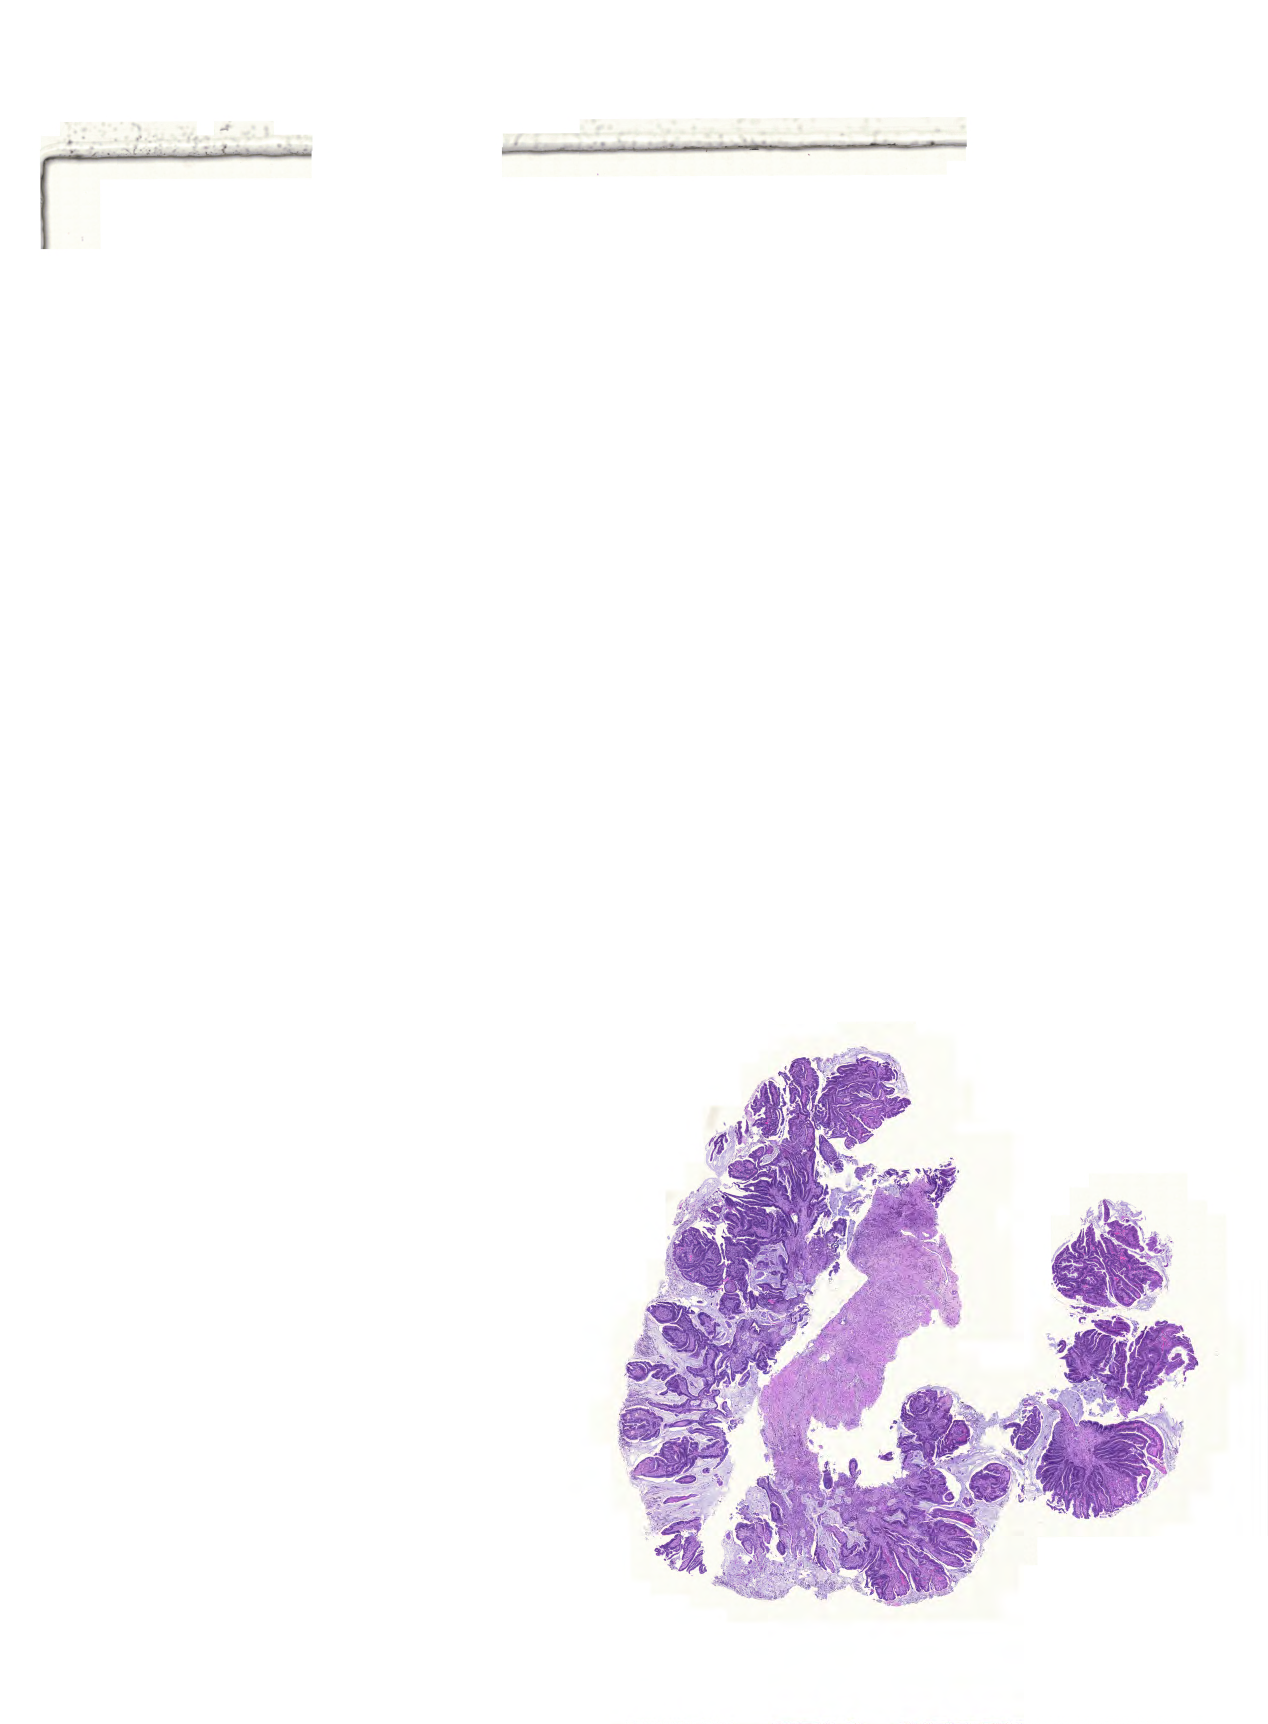
H&E whole-slide image — a low-resolution overview of the entire scanned area, about 18.9 x 25.7 mm; FFPE section; colon, primary tumour sample. Female, age 83 years at initial diagnosis.
Lymph nodes positive (case pathology): 0 of 18 examined. AJCC pathologic stage: I (6th edition). Pathologic diagnosis: Mucinous adenocarcinoma.